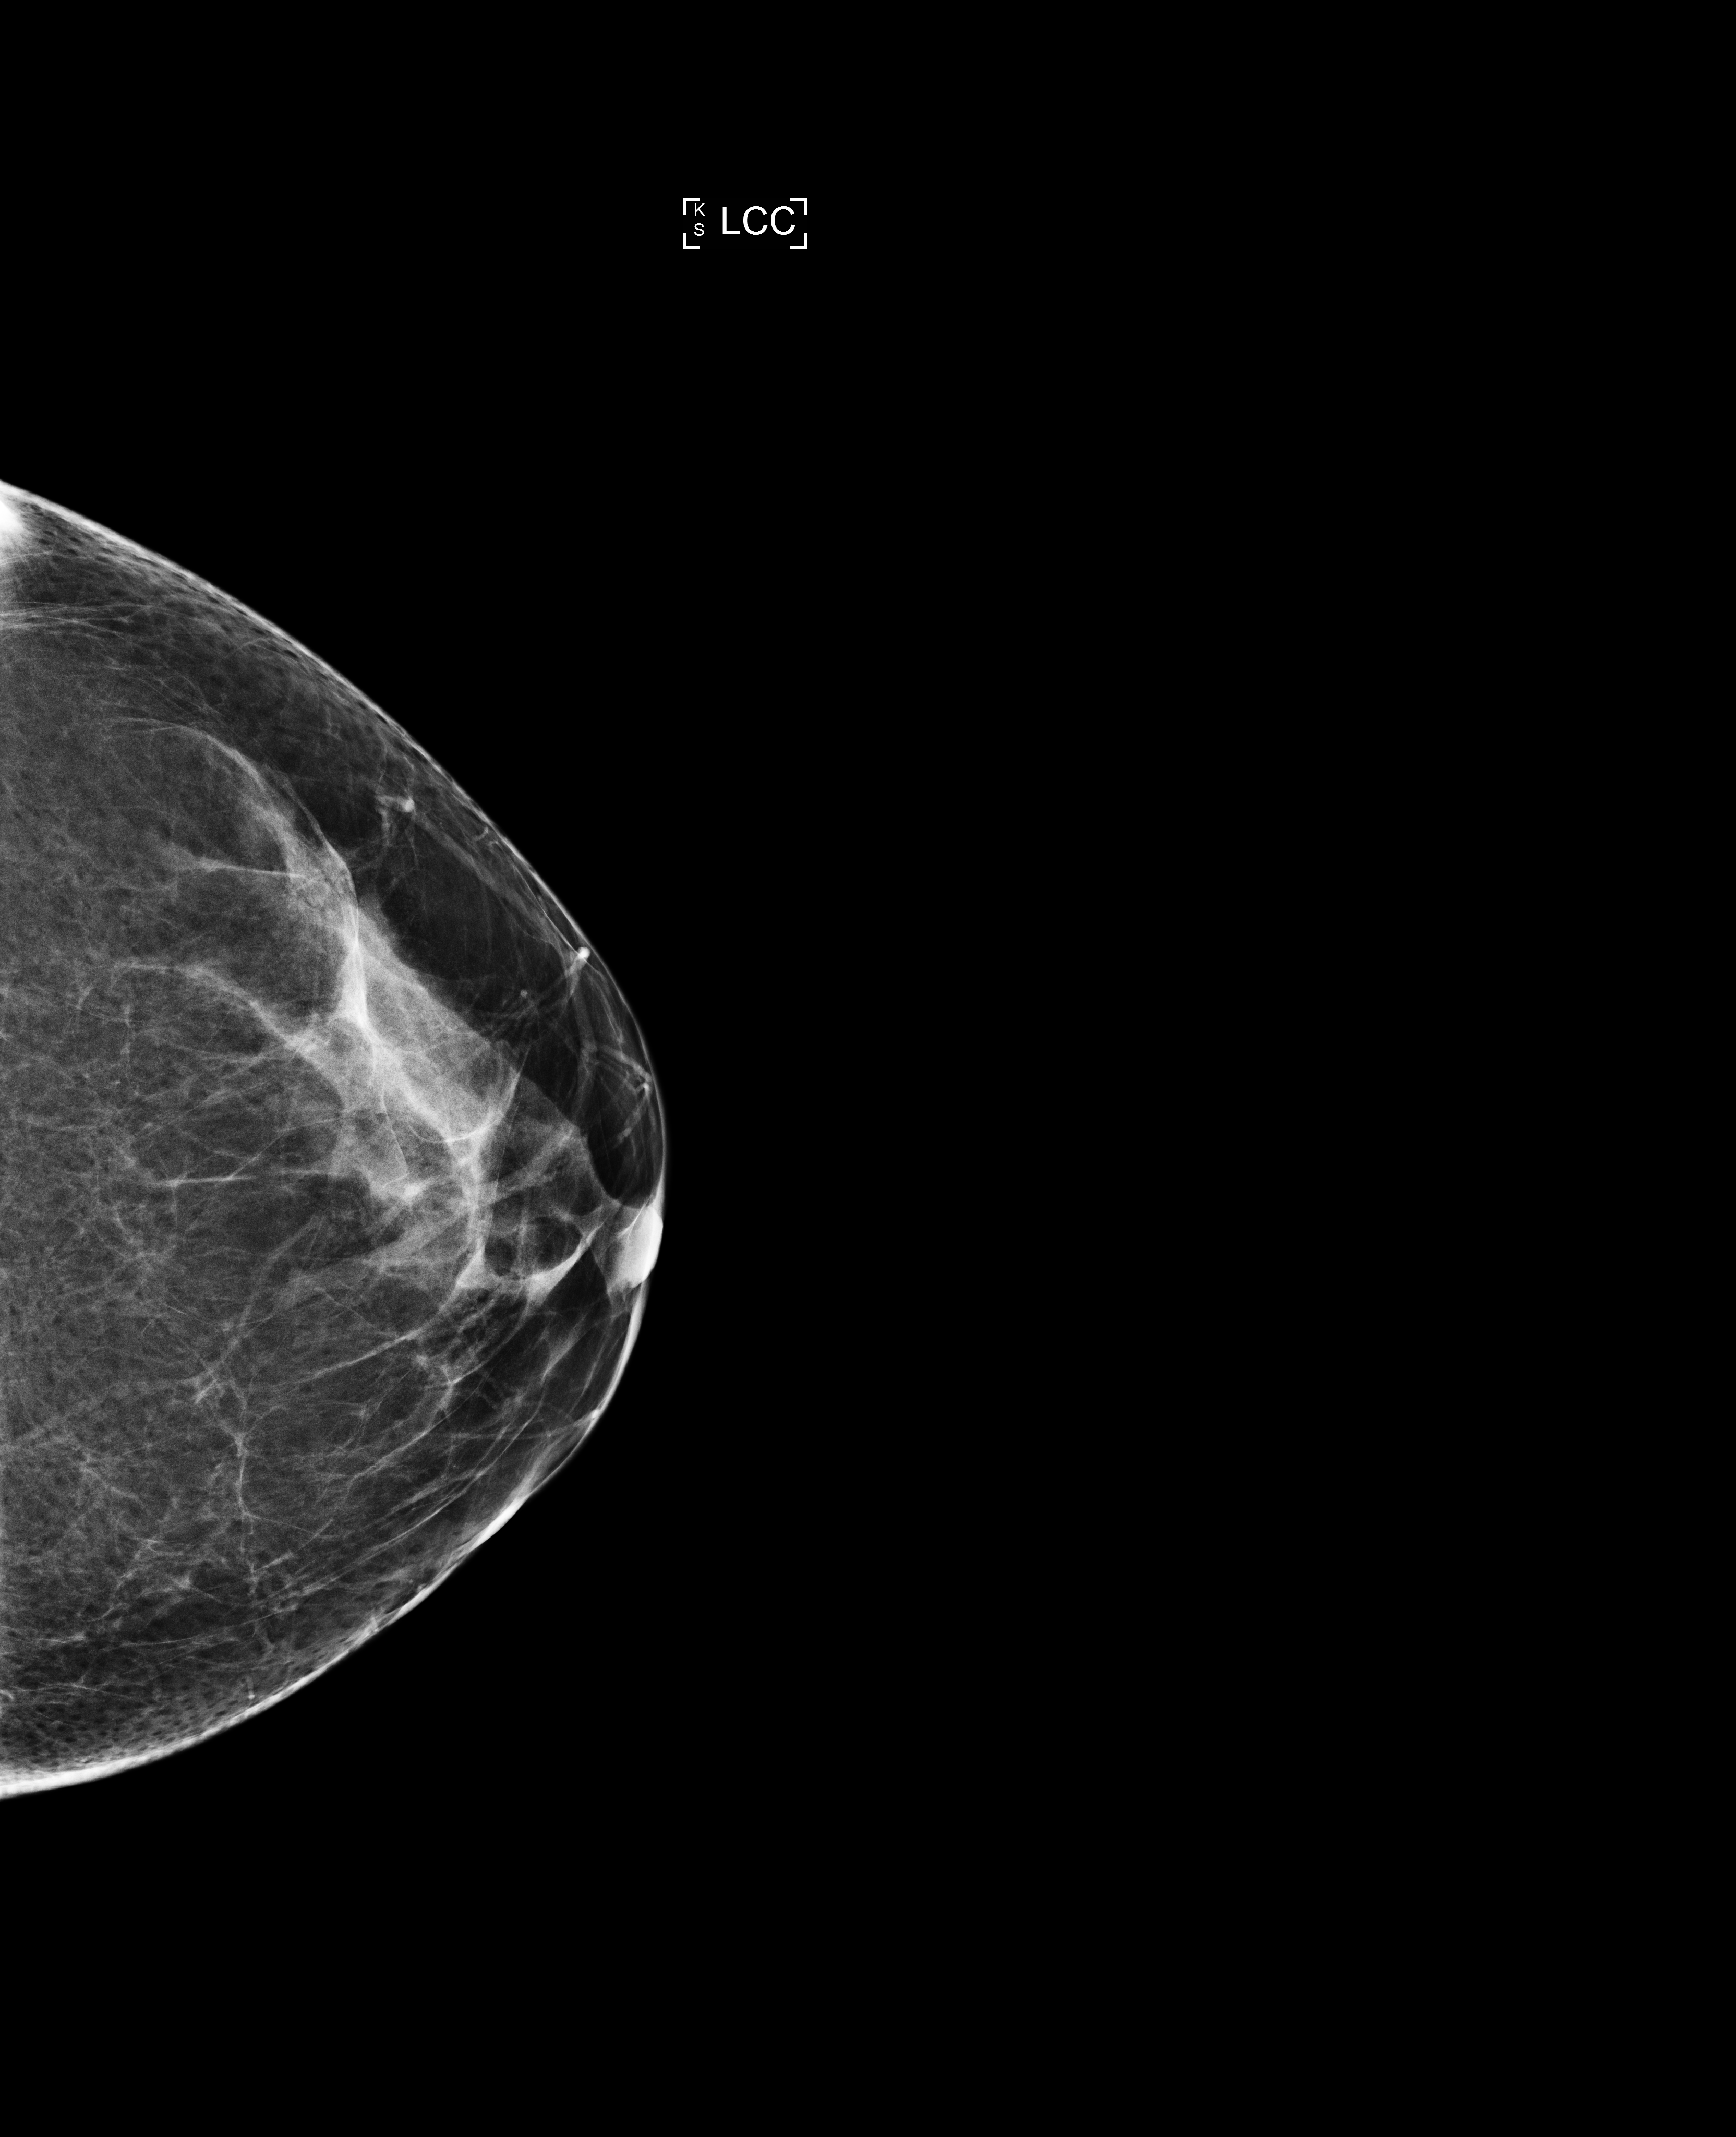
Full-field digital mammogram (FFDM), left breast, craniocaudal (CC) view, diagnostic examination (additional views). Patient: female, 49 years.
BI-RADS breast density category at the screening exam (both breasts, scale 1–4): 3. Final BI-RADS category for the screening round (tomosynthesis exam, both breasts): category 2. Recall: recalled for additional imaging after this screen.